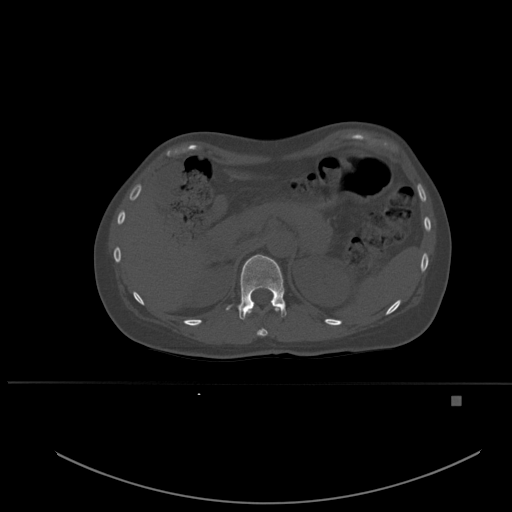
CT including the spine, one axial slice. Position 259 of 651 along the scan axis. Bone window (W 1800 / L 400 HU). 512 × 512 image matrix. Patient: female, 49 years. From the clinical record (not read from this slice): primary cancer: breast.
Structures marked on this image (semi-automatically segmented with operator editing):
- T11 vertebra: bounding box (x1, y1, x2, y2) in pixels: (247, 308, 279, 337)
- T12 vertebra: (226, 254, 287, 320)